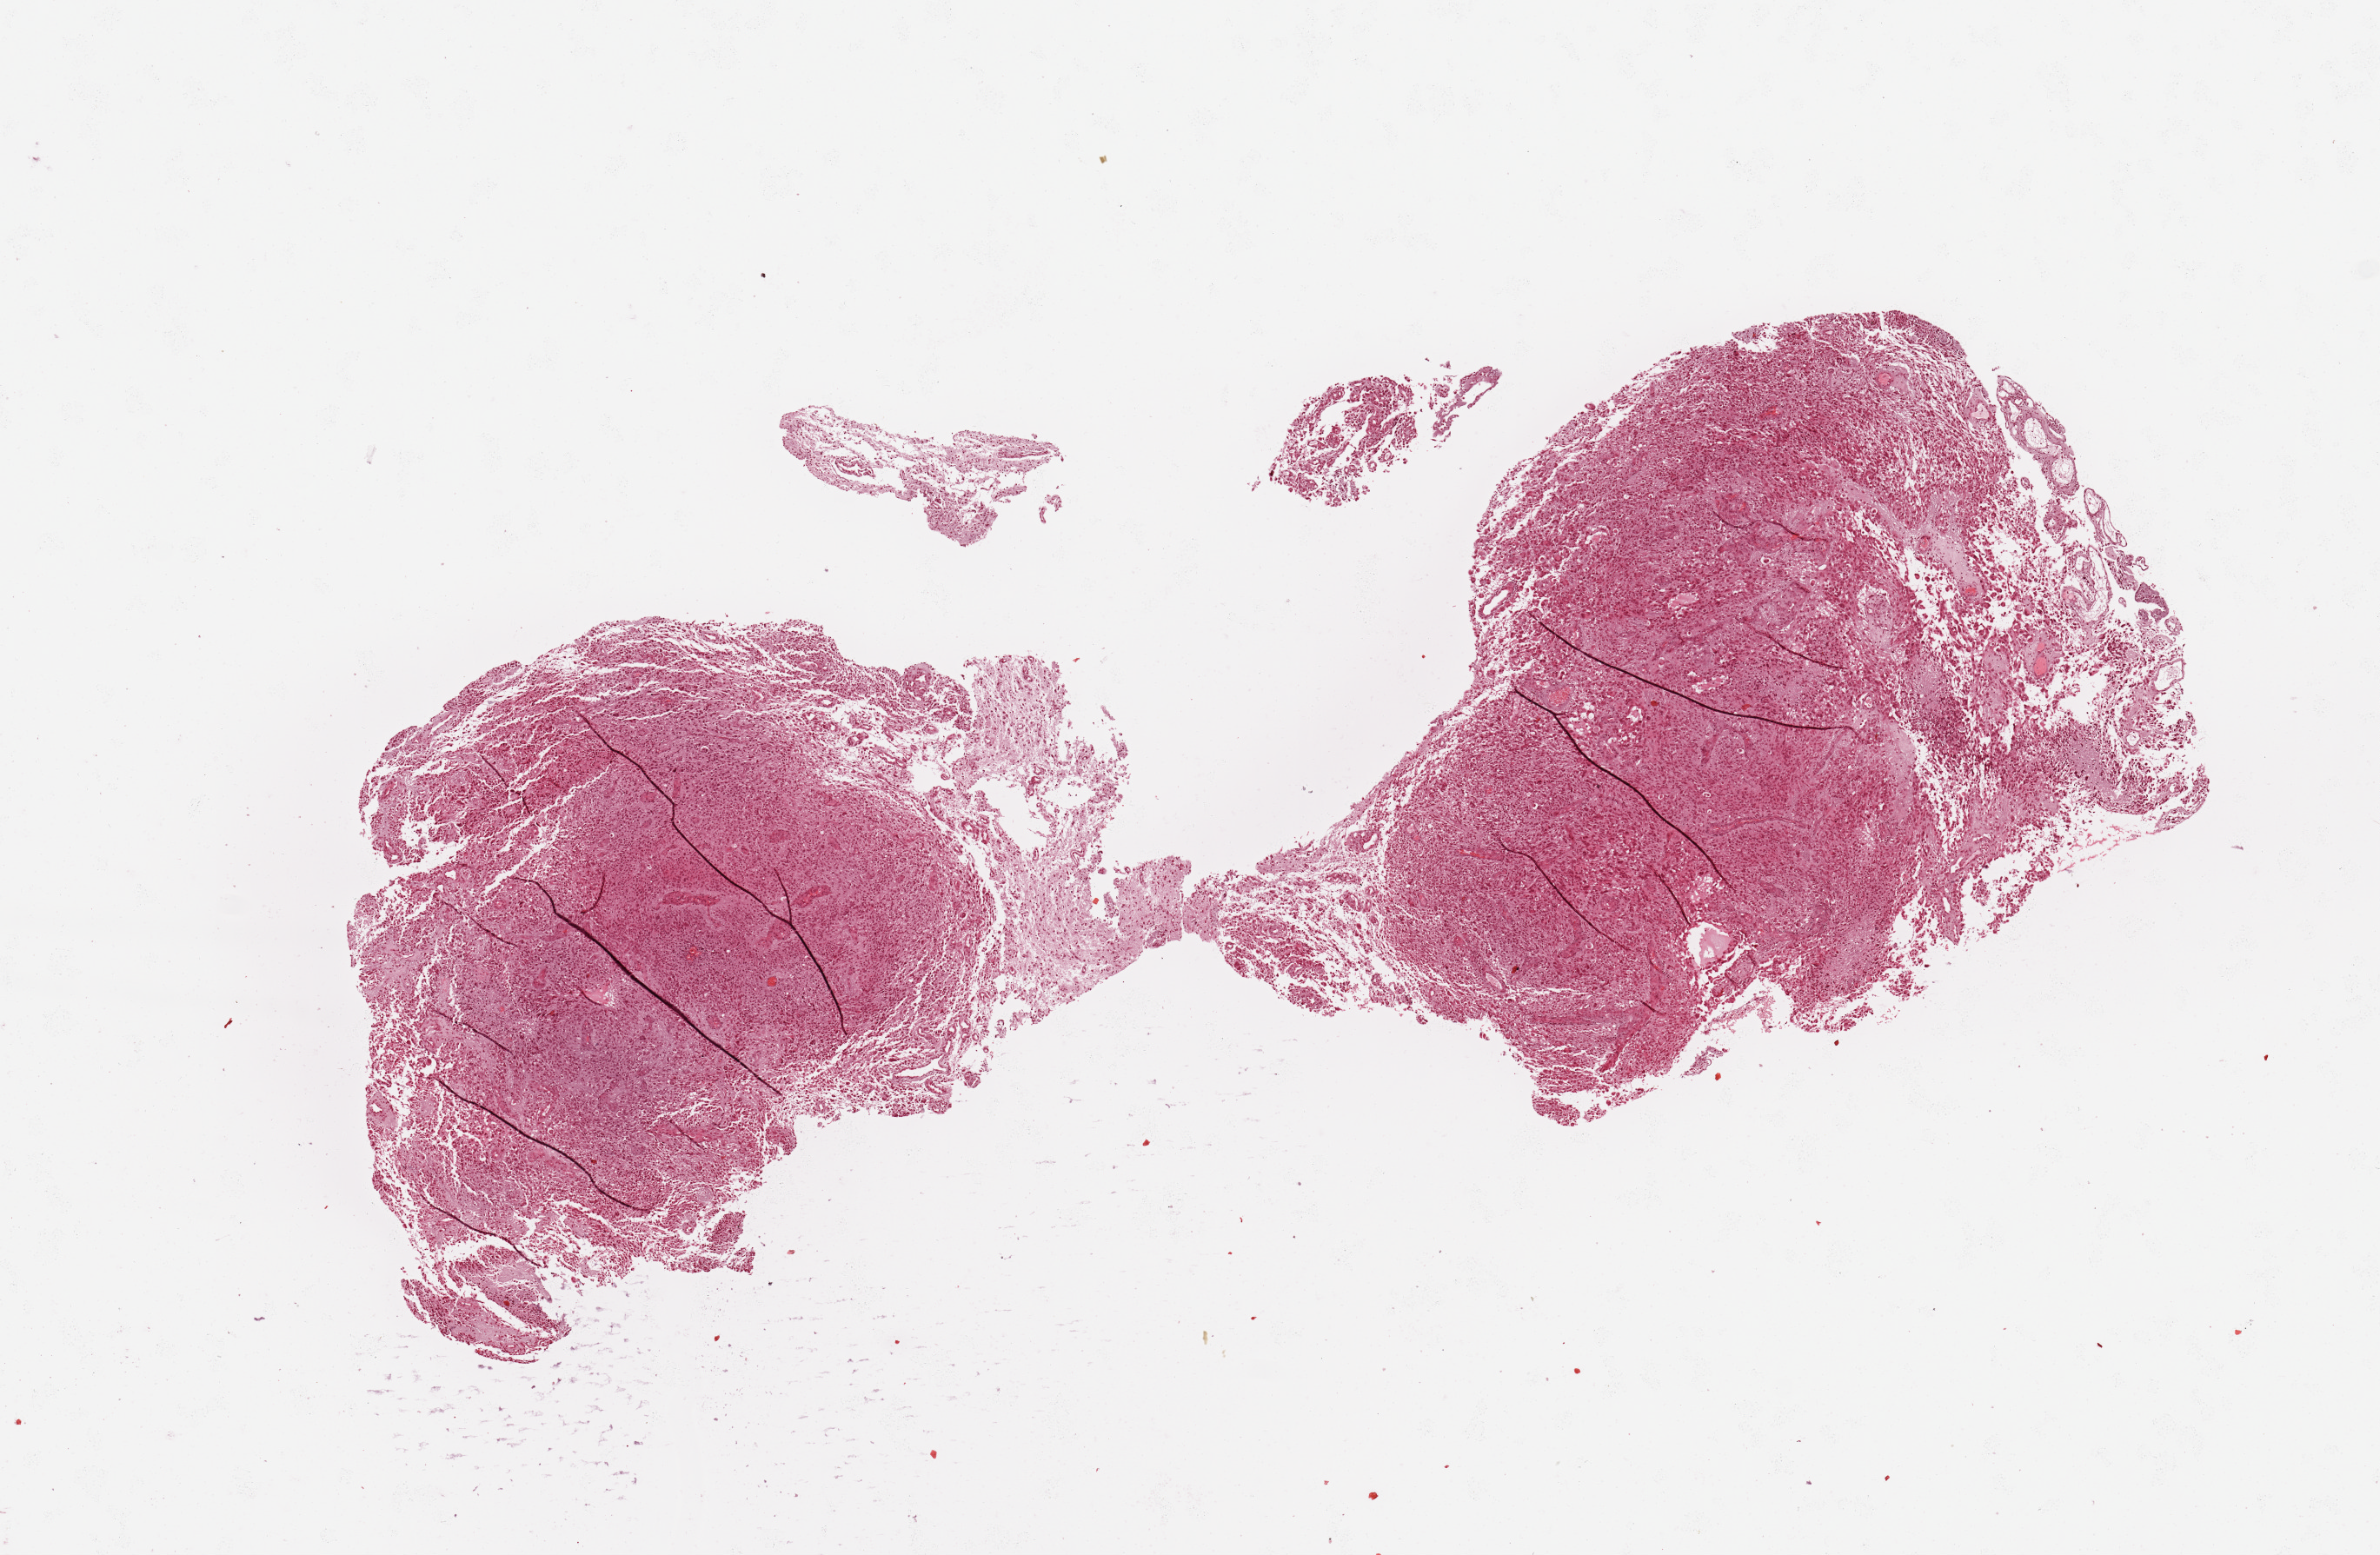
H&E whole-slide image, whole scanned area (about 10.8 x 7.1 mm) shown as a low-resolution overview; tumour tissue sample, sampled site: brain. Female, 53 y/o. Composition of this section per pathologist review: tumour nuclei 70%, necrosis 10%.
* histologic diagnosis: Glioblastoma
* primary tumour site (as recorded): temporal lobe